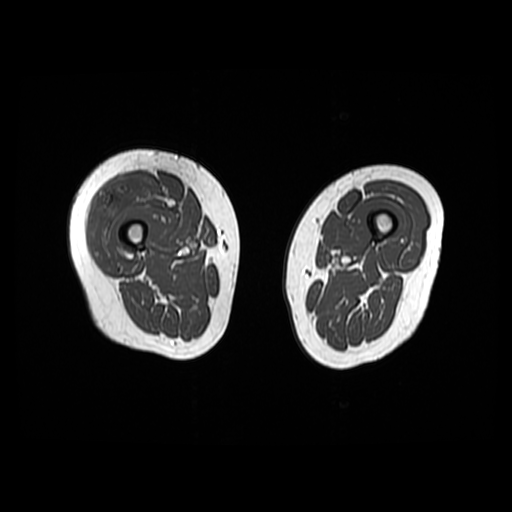
MRI of an extremity soft-tissue mass, one axial slice. 512 × 512 image matrix. Female patient. Case-level facts recorded for this patient, not image findings: histological type: pleiomorphic undifferentiated sarcoma; grade: high; site of the primary tumour: right quadricep.
Outlined on this slice (manually delineated by an expert):
- gross tumour volume including surrounding oedema: bounding box <90,174,170,258> (left, top, right, bottom; pixels)